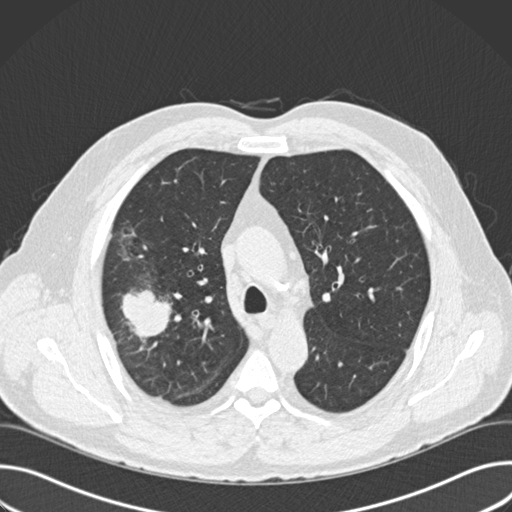
Low-dose screening chest CT, one axial slice. Slice 112 of 157 in the series (ordered by position). Reconstruction kernel B30f. Lung window (W 1500 / L -600 HU). 512 × 512 image matrix, field of view 380 × 380 mm.
Annotated regions visible in this slice (outlined manually by an expert reader):
- lesion 1 (tumor, upper lobe of right lung): bounding box (x1, y1, x2, y2) in pixels: (121, 290, 172, 342)